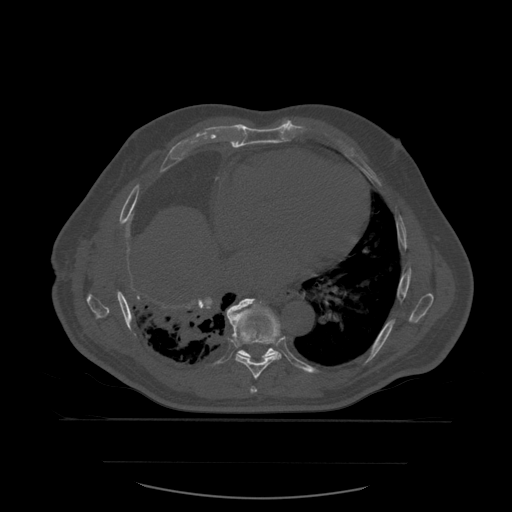
CT including the spine, one axial slice. Position 355 of 590 along the scan axis. Bone window (W 1800 / L 400 HU). 512 × 512 image matrix, field of view 479 × 479 mm. Patient age 71 years. From the clinical record (not read from this slice): primary cancer: lung.
Annotated regions visible in this slice (semi-automatically segmented with operator editing):
- T7 vertebra: box from (x=251, y=387) to (x=258, y=393) px
- T8 vertebra: (x=227, y=299)–(x=282, y=380)
- T9 vertebra: (x=239, y=299)–(x=281, y=358)